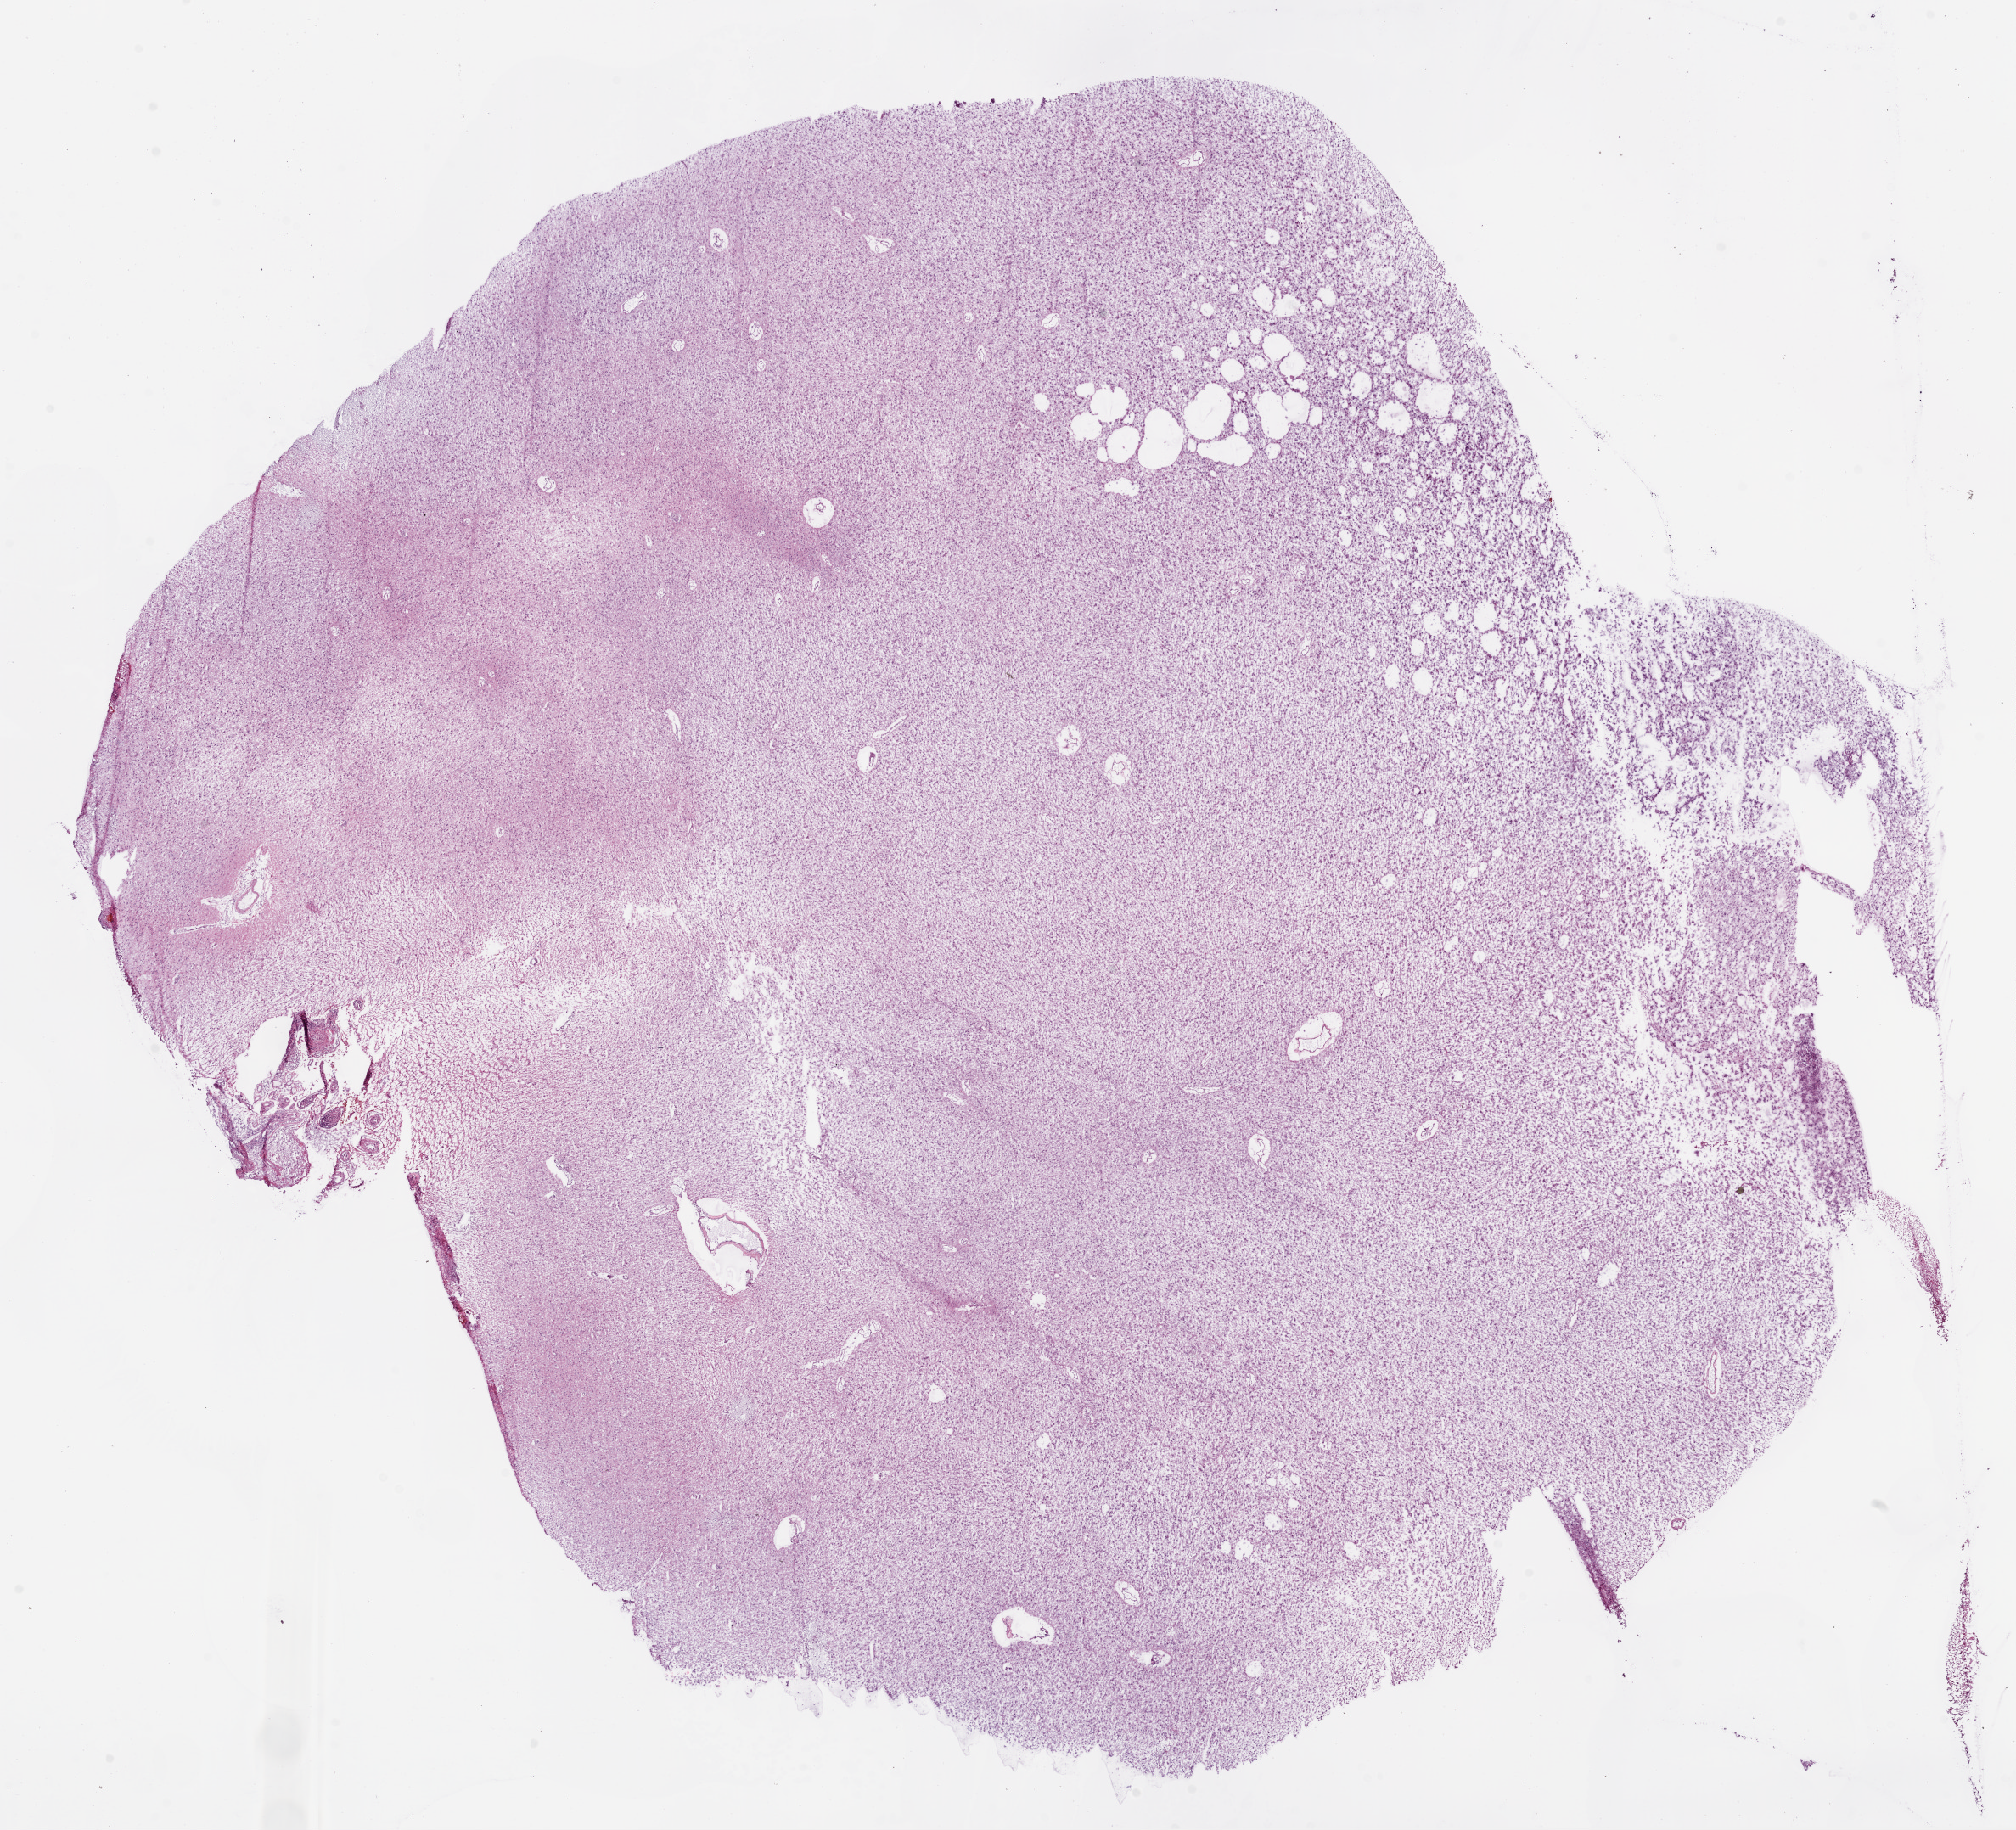
Digitized Hematoxylin and eosin (H&E) stained tissue section (whole slide) — low-resolution overview of the scanned area, about 19.1 x 17.3 mm (slide scanned at 20x); frozen section; brain, primary tumour sample. Male, age 43 years at initial diagnosis. Histologic grade: G2 (moderately differentiated). Pathologist review of this section (percent, as recorded): tumour cells 100%, tumour nuclei 65%, normal cells 0%, stromal cells 0%, necrosis 0%.
Pathologic diagnosis: Mixed glioma (cerebrum).